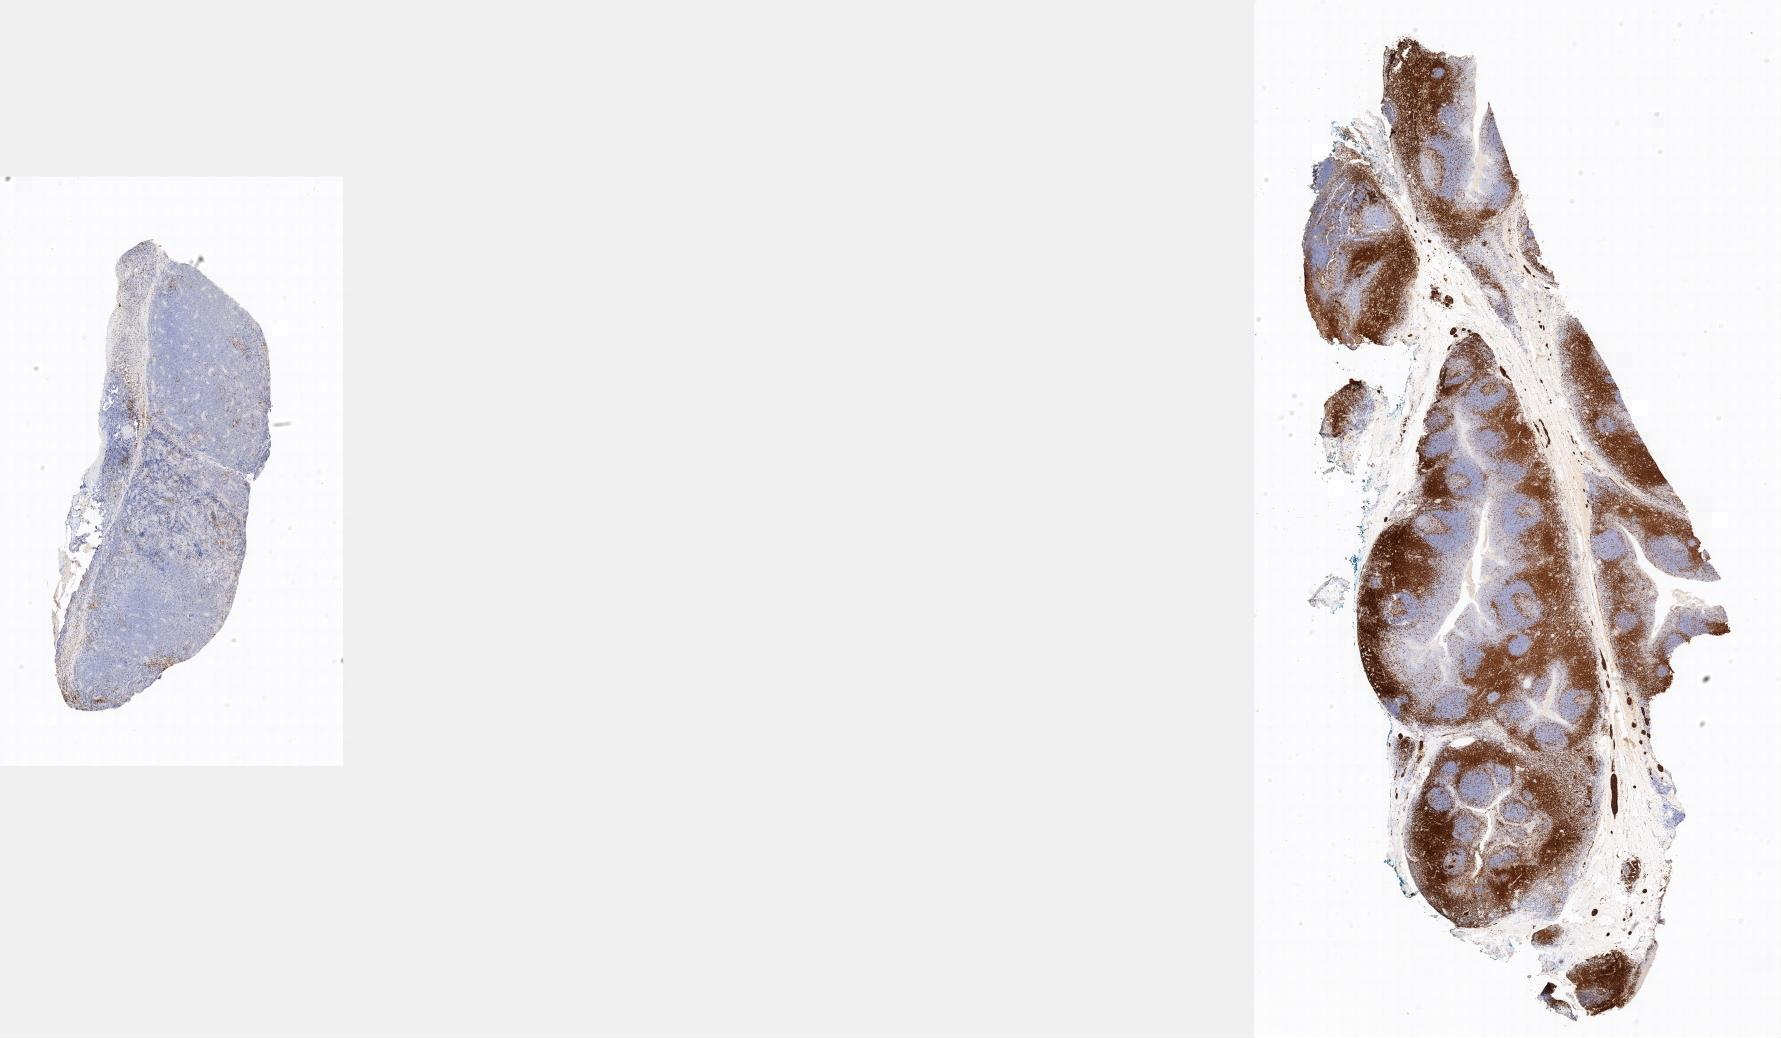
Whole-slide image, immunohistochemical stain for CD3, a low-resolution overview of the entire scanned area; specimen: tumor tissue; site: testis. Male patient; age at initial diagnosis 8 years.
Diagnosis: Burkitt lymphoma, NOS.